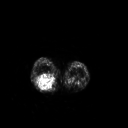
FDG PET of an extremity soft-tissue mass (from a PET/CT study), one axial slice; position 172 of 267 along the scan axis; 3.27 mm slice thickness; 128 × 128 image matrix. Female patient, age 62 years. Case-level facts recorded for this patient, not image findings: histological type: liposarcoma; site of the primary tumour: right thigh.
Annotated regions visible in this slice (expert contour drawn on MRI and transferred to this co-registered scan by the dataset authors):
- gross tumour volume (mass): bounding box <37,73,56,90> (left, top, right, bottom; pixels)